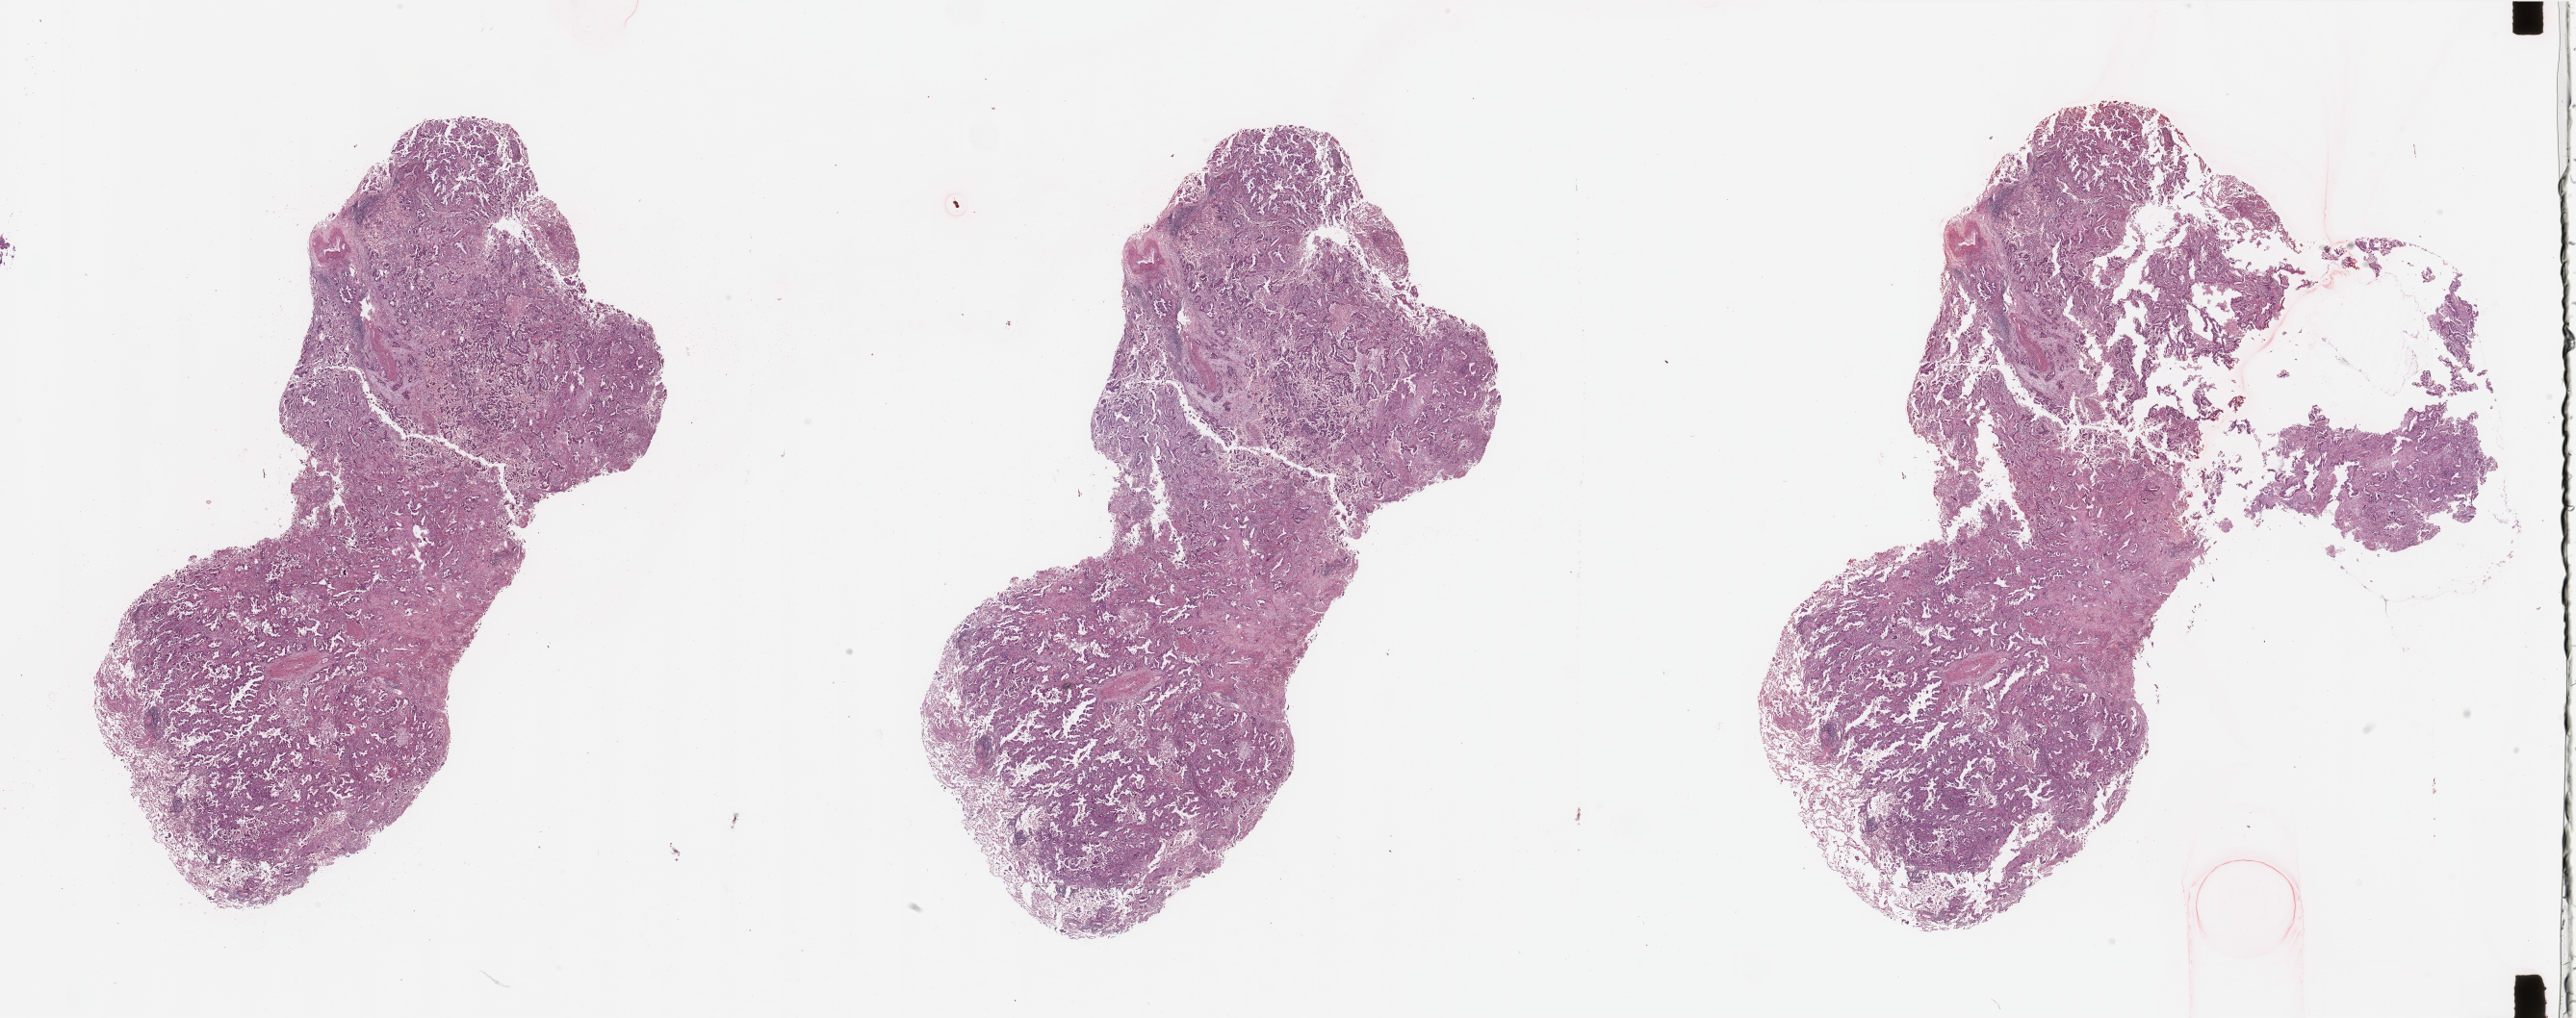
Whole-slide histology image, H&E, shown as a low-resolution overview of the whole scanned area (about 42.3 x 16.7 mm, from a 20x scan); tumour tissue sample, sampled site: lung. Female, 73 y/o. Histologic grade: G2 (moderately differentiated). Slide review estimates, as recorded: tumour nuclei 80%, necrosis 3%.
Diagnosis: Adenocarcinoma, NOS. AJCC pathologic stage: IIIA.